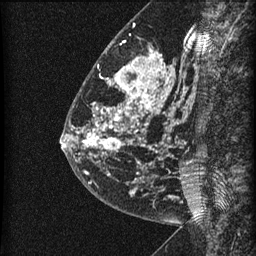
Breast MRI (dynamic contrast-enhanced), one sagittal slice; slice 21 of 60 in the series (ordered by position); dynamic contrast-enhanced series, image 2 of 3 at this slice position (ordered by acquisition); 1.5 T; TE 4.2 ms, TR 22.7 ms; 1.5 mm slice thickness; 256 × 256 image matrix, field of view 180 × 180 mm. Patient: female, 48 years. Case-level facts recorded for this patient, not image findings: setting: breast cancer imaged before/during neoadjuvant chemotherapy; receptor status: triple-negative.
Annotated regions visible in this slice (semi-automatic segmentation, software-assisted and operator-edited):
- analysis volume of interest (the breast-tissue region the enhancement analysis was run in; not a lesion): bounding box (x1, y1, x2, y2) in pixels: (81, 23, 186, 202)
- tumour enhancement mask (voxels above the 90 % enhancement threshold inside the analysis volume of interest): (82, 54, 172, 172)